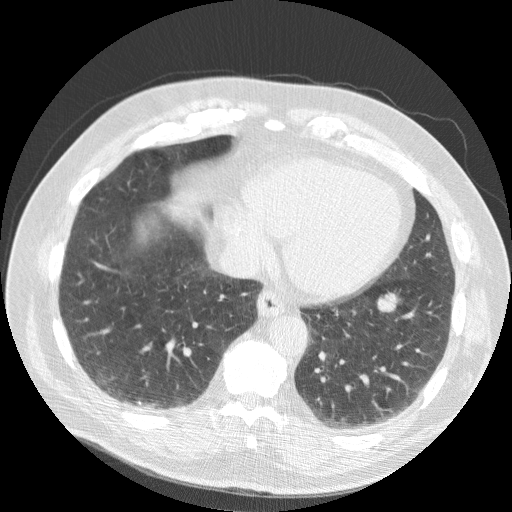
Low-dose screening chest CT, axial slice. Second annual screen. Lung window (W 1500 / L -600 HU). 2.5 mm slice thickness. Slice 74 of 188 in the series. Male, age 63 years at enrolment.
• Lesion marked by an expert reader, bounding box (x1, y1, x2, y2) in pixels: (362, 287, 410, 325).
• The screening reader recorded 2 non-calcified nodules or masses ≥4 mm on this exam (right middle lobe, left lower lobe); which of them this box marks is not recorded.
• Official screen result: positive, change unspecified: nodule(s) >= 4 mm or enlarging nodule(s), mass(es), or other non-specific abnormalities suspicious for lung cancer.